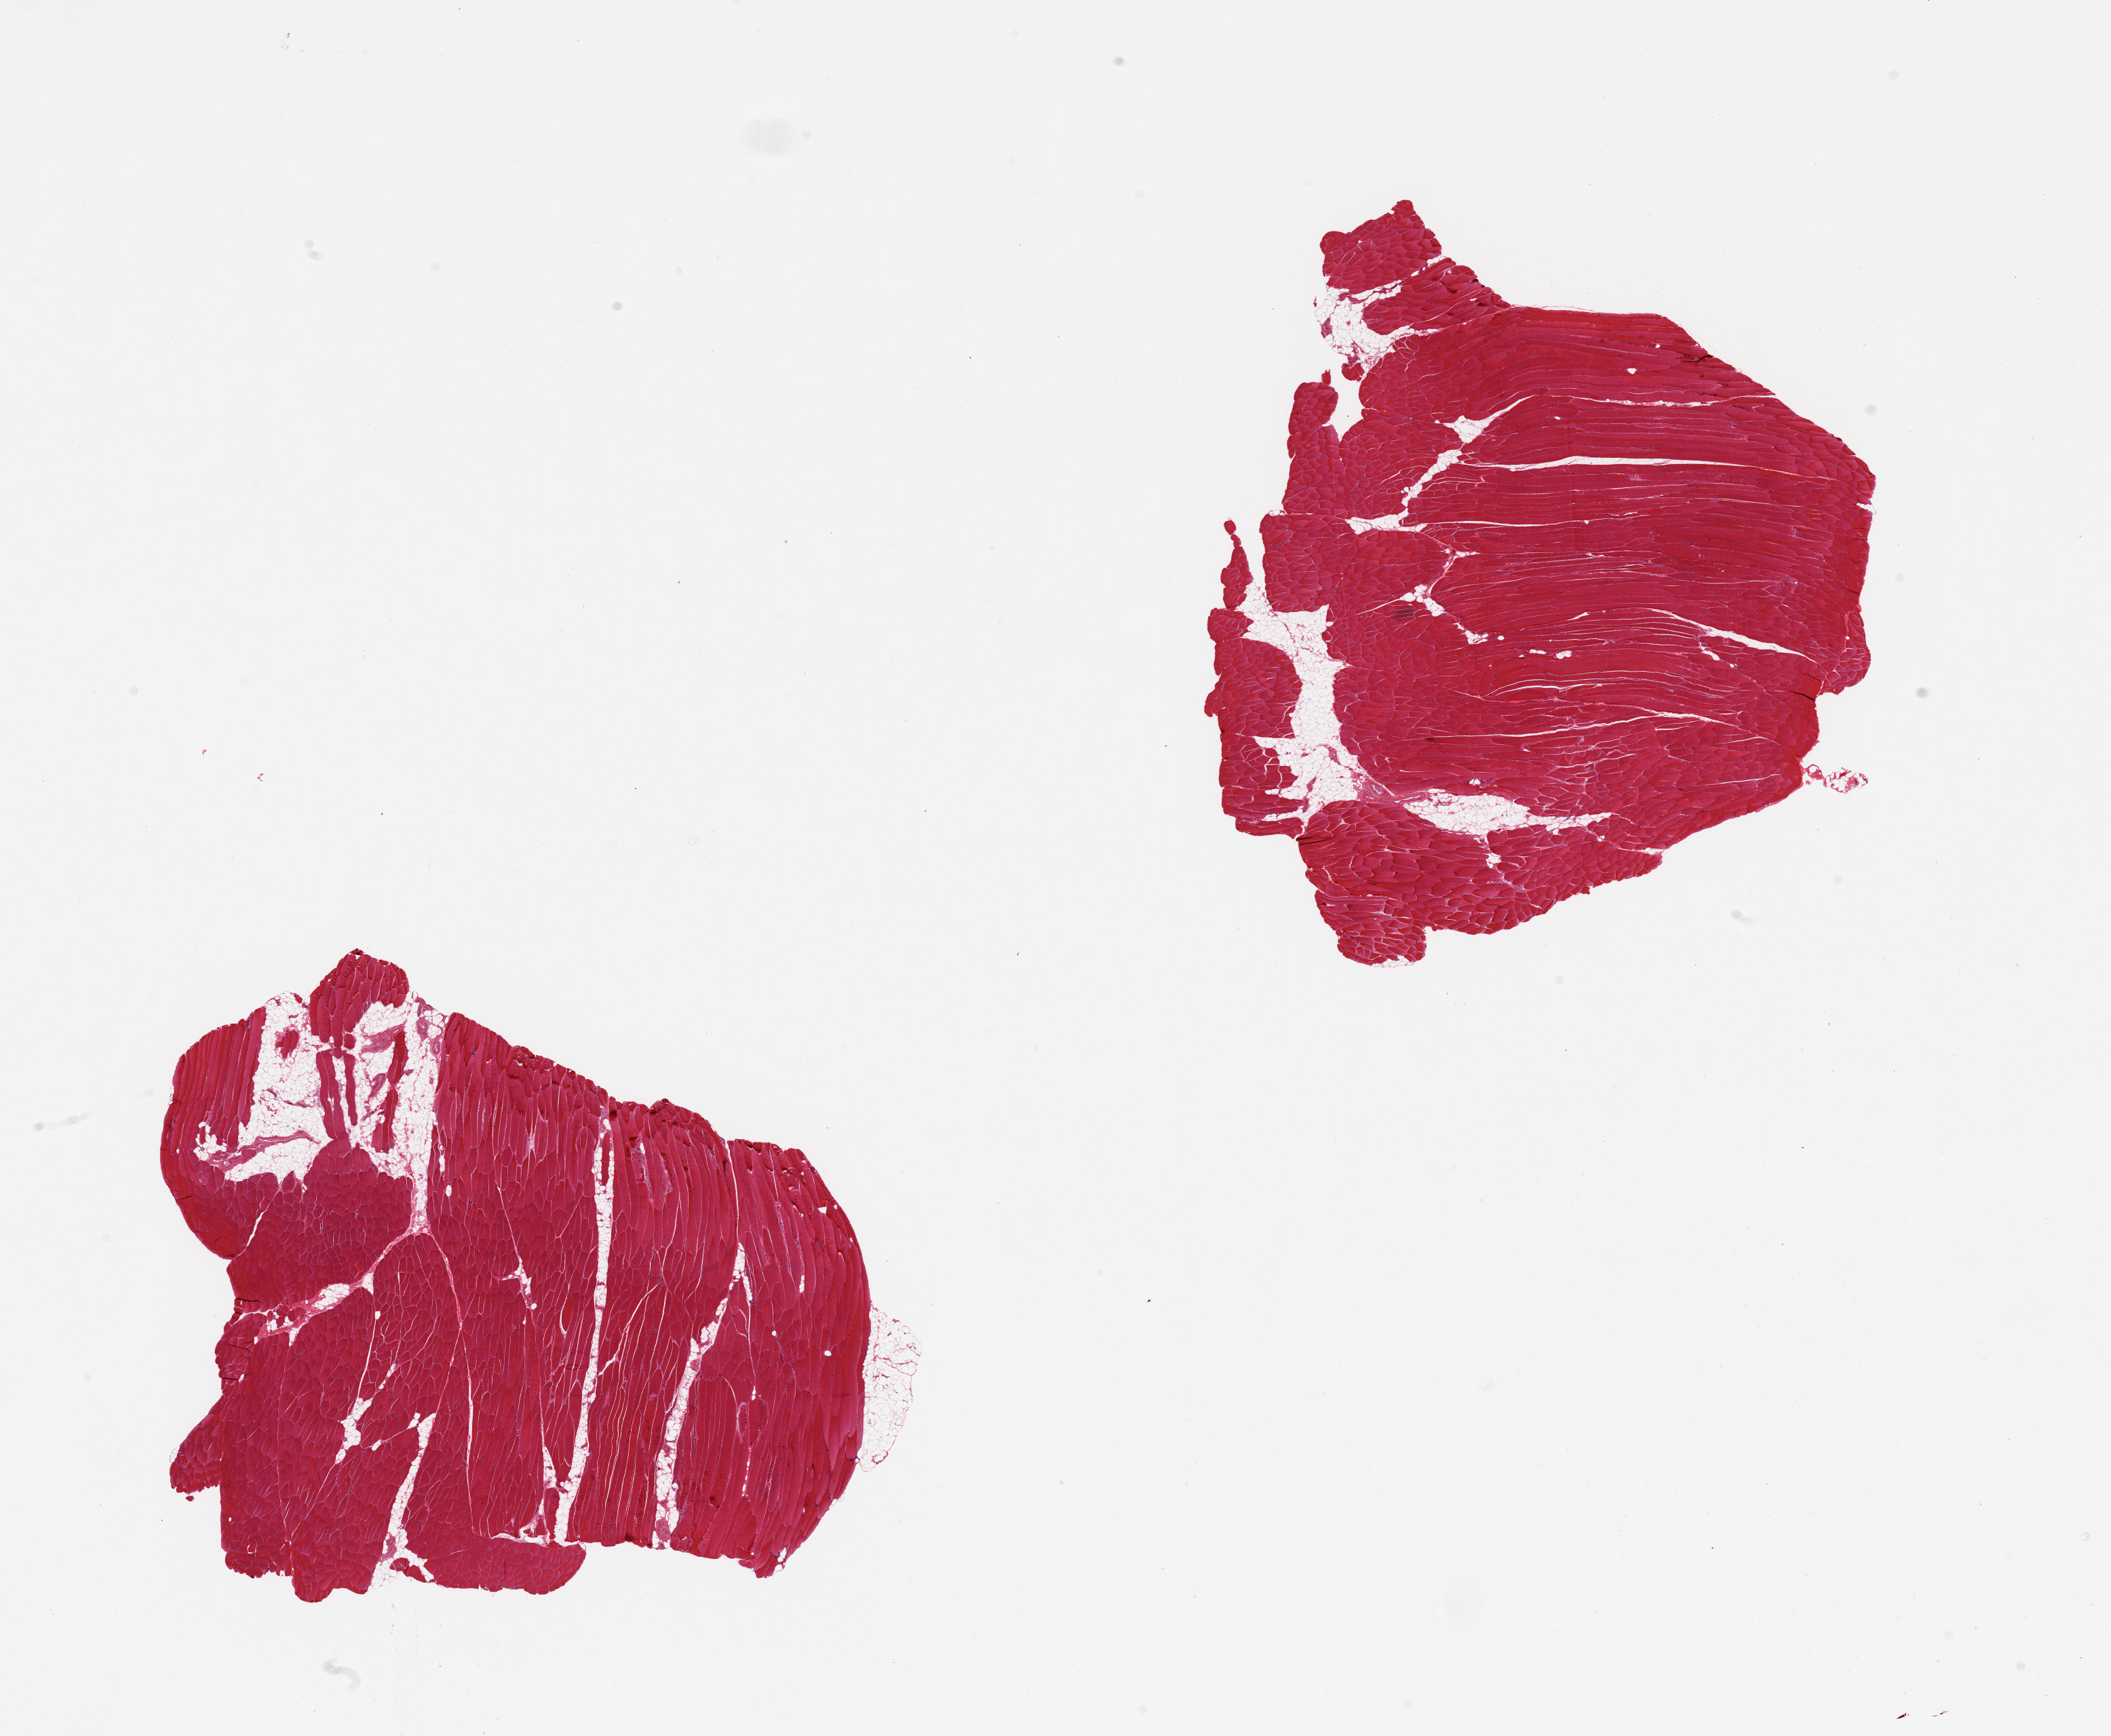
Whole-slide image, H&E stain — shown as a low-resolution overview of the whole scanned area (about 24.6 x 20.2 mm, from a 20x scan), PAXgene-fixed, paraffin-embedded tissue, sampled site (target tissue): skeletal muscle, donor tissue sample. Male donor.
Pathologist's review note for this sample: 2 pieces; 10% internal fat.